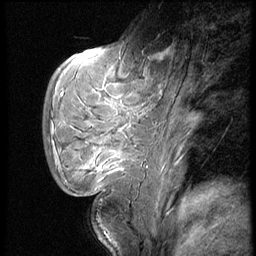
Breast MRI (dynamic contrast-enhanced), one sagittal slice; slice 18 of 62 in the series (ordered by position); dynamic contrast-enhanced series, image 2 of 4 at this slice position (ordered by acquisition); 1.5 T; TE 4.2 ms, TR 9 ms; 2.5 mm slice thickness; 256 × 256 image matrix. Female patient, age 28 years. Case-level facts recorded for this patient, not image findings: setting: breast cancer imaged before/during neoadjuvant chemotherapy.
Outlined on this slice (semi-automatic segmentation, software-assisted and operator-edited):
- analysis volume of interest (the breast-tissue region the enhancement analysis was run in; not a lesion): bounding box [x1, y1, x2, y2] px = [48, 54, 150, 183]
- tumour enhancement mask (voxels above the 140 % enhancement threshold inside the analysis volume of interest): [84, 164, 125, 170]